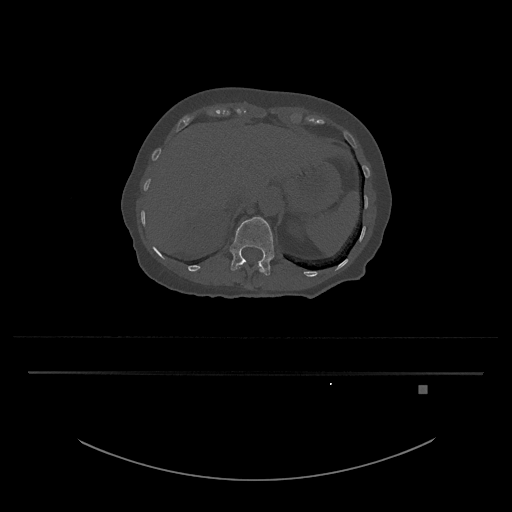
CT including the spine, one axial slice. Slice 572 of 797 in the series (ordered by position). Reconstruction kernel Br40s/3. Bone window (W 1800 / L 400 HU). 0.5 mm slice thickness. 512 × 512 image matrix, field of view 500 × 500 mm. Patient: female, 57 years. Case-level facts recorded for this patient, not image findings: primary cancer: cervical.
Annotated regions visible in this slice (semi-automatically segmented with operator editing):
- L1 vertebra: box from (x=230, y=217) to (x=274, y=276) px
- T12 vertebra: (x=237, y=262)–(x=264, y=273)